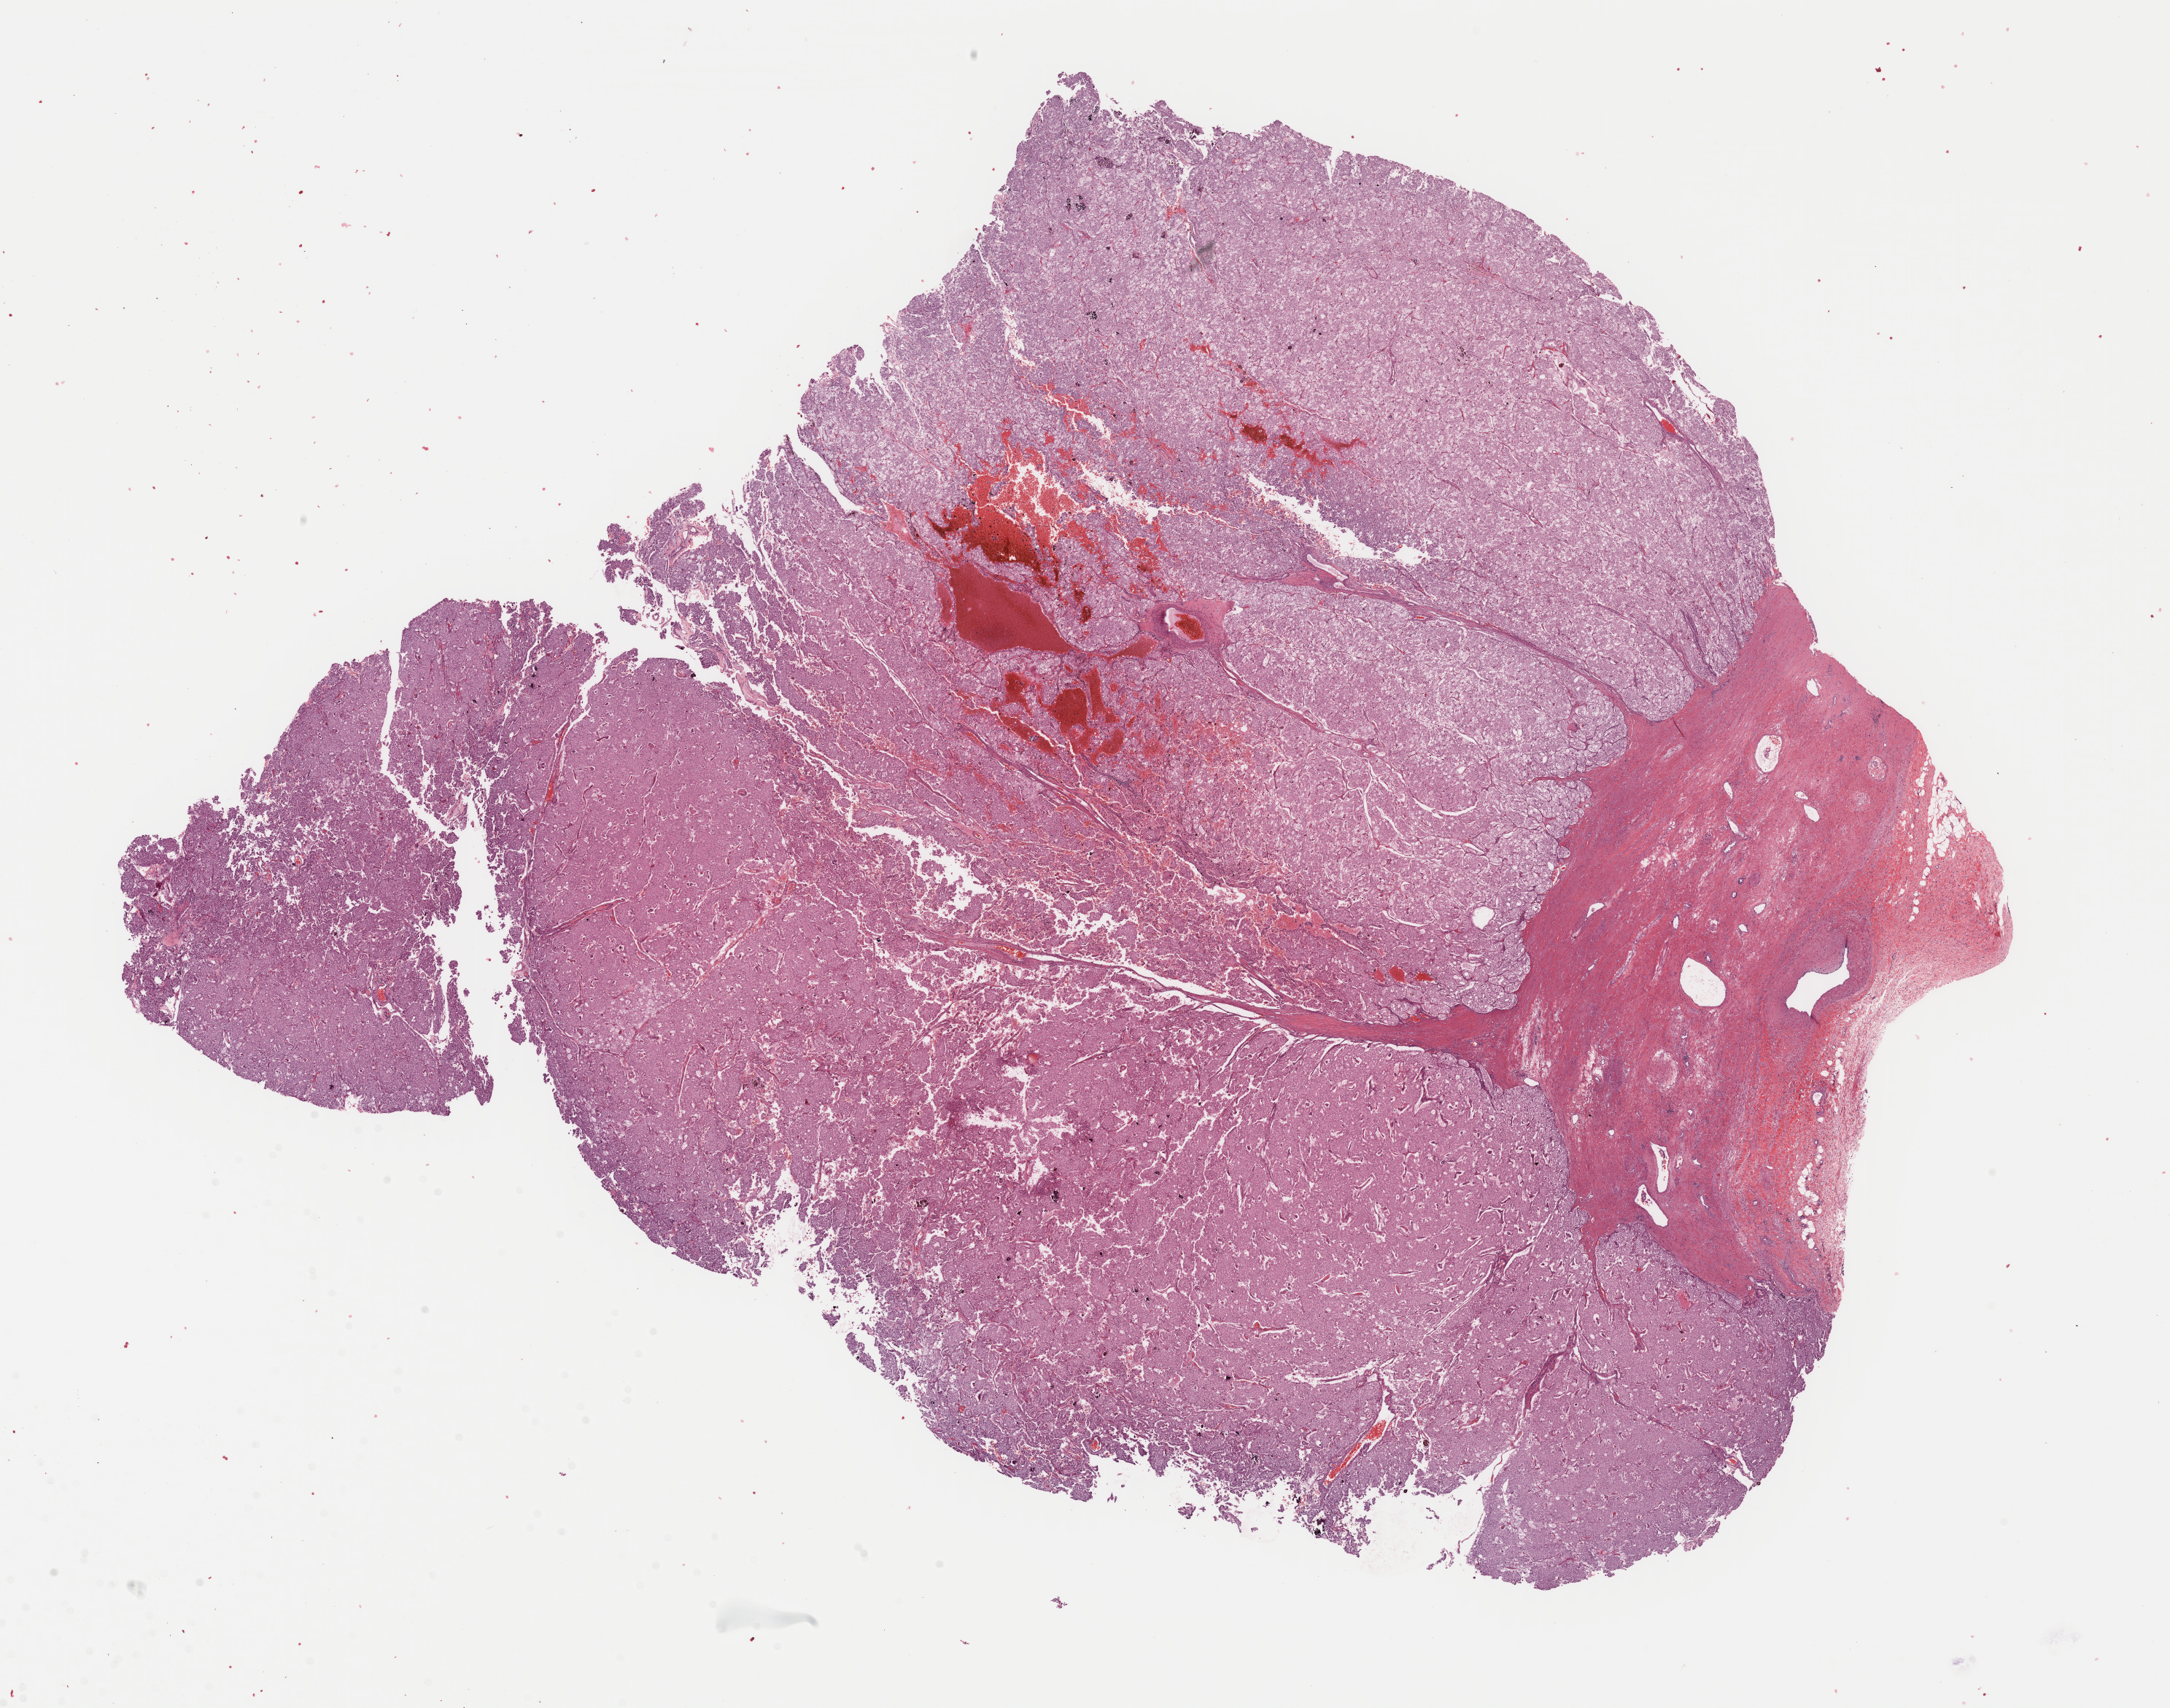
H&E-stained whole-slide image, a low-resolution overview of the entire scanned area, about 23.5 x 18.5 mm (from a 40x scan). Formalin-fixed paraffin-embedded (FFPE) diagnostic section. Primary tumour sample from the kidney. Male patient; age at initial diagnosis 42 years.
Laterality: left. AJCC pathologic stage: II (7th edition). Histologic diagnosis: Renal cell carcinoma, chromophobe type. TNM: T2 N0 M0.